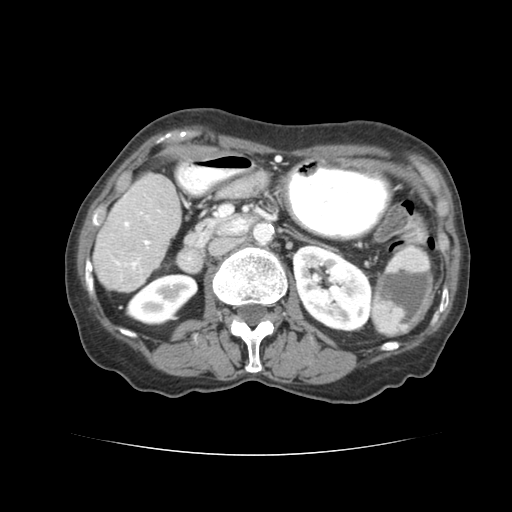
Contrast-enhanced abdominal CT (liver protocol), one axial slice; position 21 of 77 along the scan axis; reconstruction kernel STANDARD; soft-tissue window (W 400 / L 40 HU); 2.5 mm slice thickness; 512 × 512 image matrix, field of view 340 × 340 mm. Case-level facts recorded for this patient, not image findings: diagnosis: hepatocellular carcinoma (patient treated with transarterial chemoembolisation; whether this scan precedes or follows treatment is not stated here); TNM stage (as recorded): Stage-I; Child-Pugh class: A; tumour differentiation: well differentiated; tumour nodularity: uninodular.
Structures marked on this image (semi-automatically segmented with operator editing):
- liver parenchyma outside the tumour (the mass and vessels are separate outlines, so this box may not span the whole liver): box from (x=92, y=170) to (x=178, y=288) px
- liver vessels: (x=96, y=191)–(x=158, y=268)